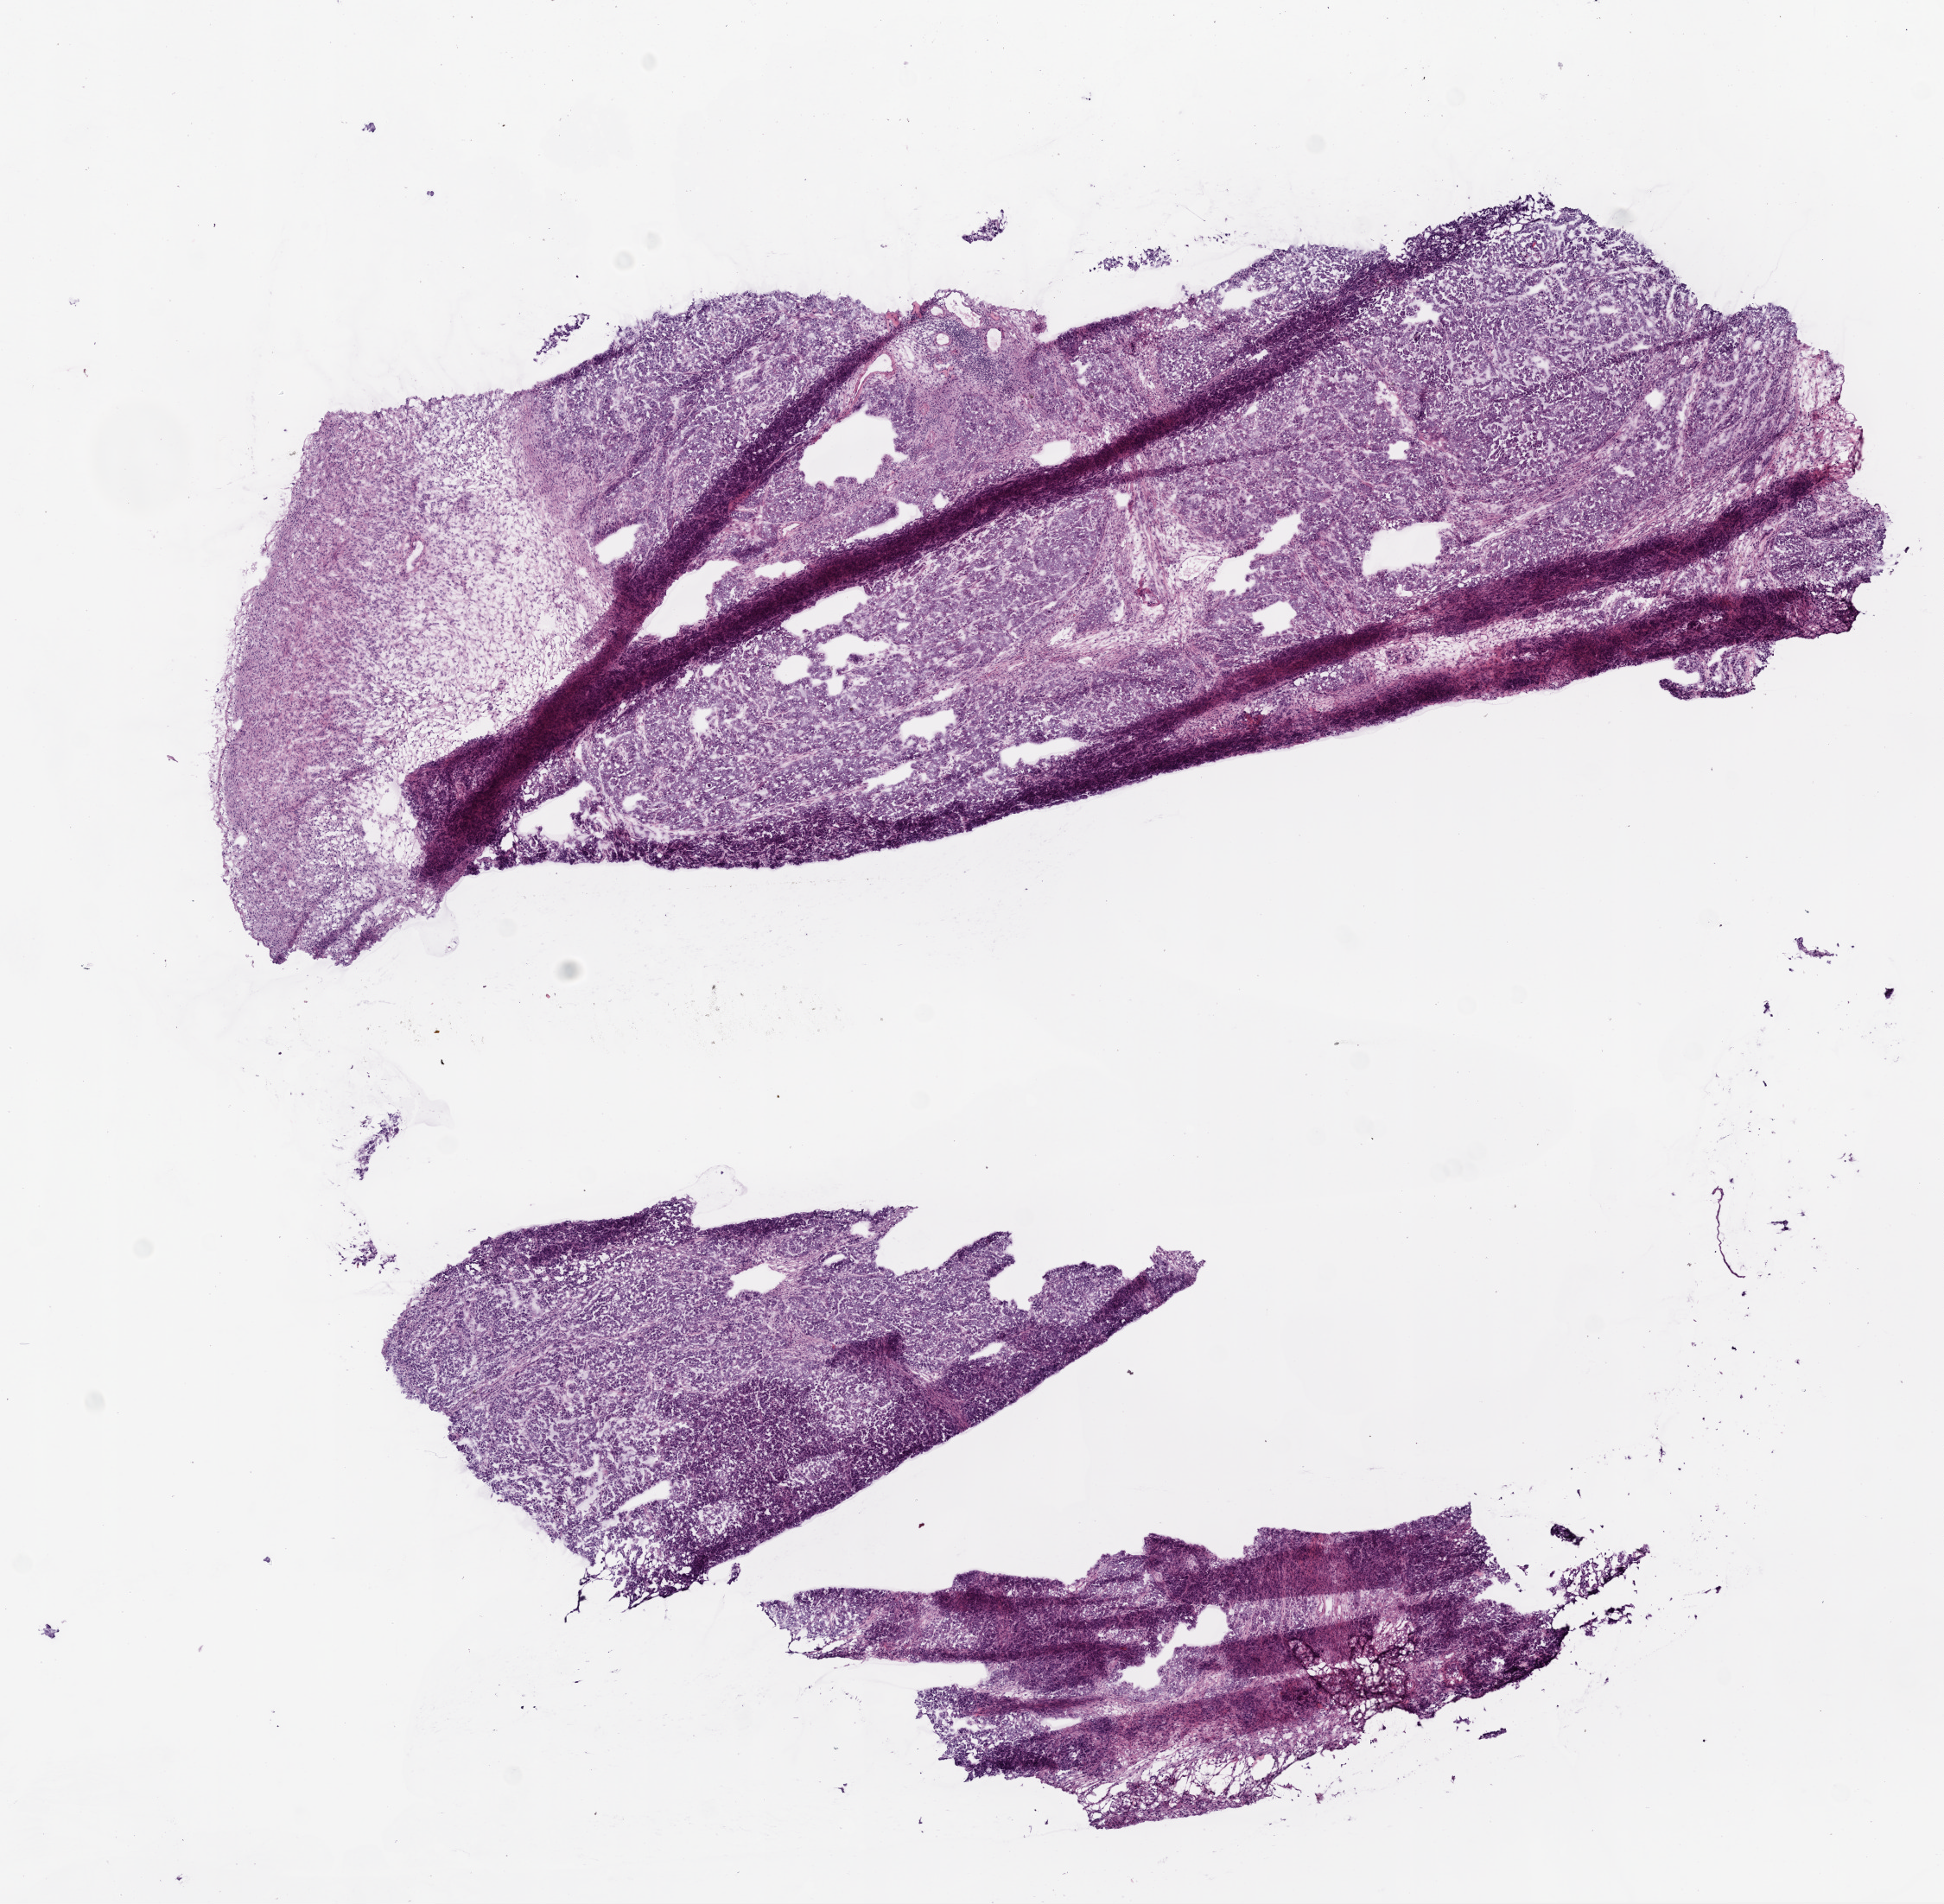
Whole-slide histology image, H&E — whole scanned area (about 9.0 x 8.8 mm) shown as a low-resolution overview. Frozen section. Ovary, primary tumour sample. Female patient; age at initial diagnosis 45 years. Histologic grade: G3 (poorly differentiated). Composition of this section per pathologist review: tumour cells 90%, tumour nuclei 90%, normal cells 1%, stromal cells 9%, necrosis 0%.
* FIGO stage: IV
* laterality: right
* pathologic diagnosis: Serous cystadenocarcinoma, NOS